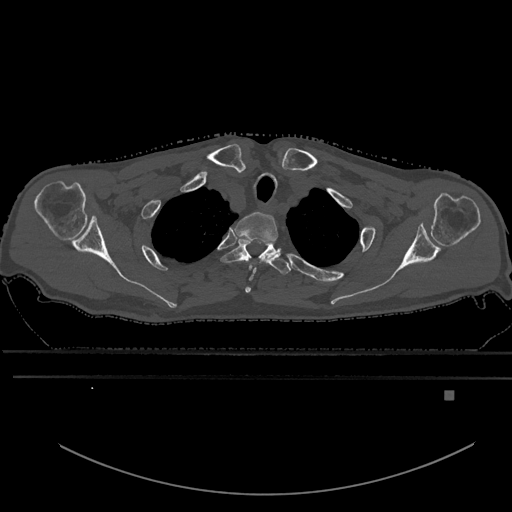
CT including the spine, one axial slice; slice 510 of 969 in the series (ordered by position); bone window (W 1800 / L 400 HU); 0.5 mm slice thickness; 512 × 512 image matrix, field of view 456 × 456 mm. Male patient, age 82 years. Case-level facts recorded for this patient, not image findings: primary cancer: prostate; vertebrae with lytic lesions (as recorded): T11, T9, T8, T2.
Structures marked on this image (semi-automatic segmentation, software-assisted and operator-edited):
- T1 vertebra: box from (x=234, y=212) to (x=278, y=293) px
- T2 vertebra: (x=221, y=239)–(x=290, y=275)